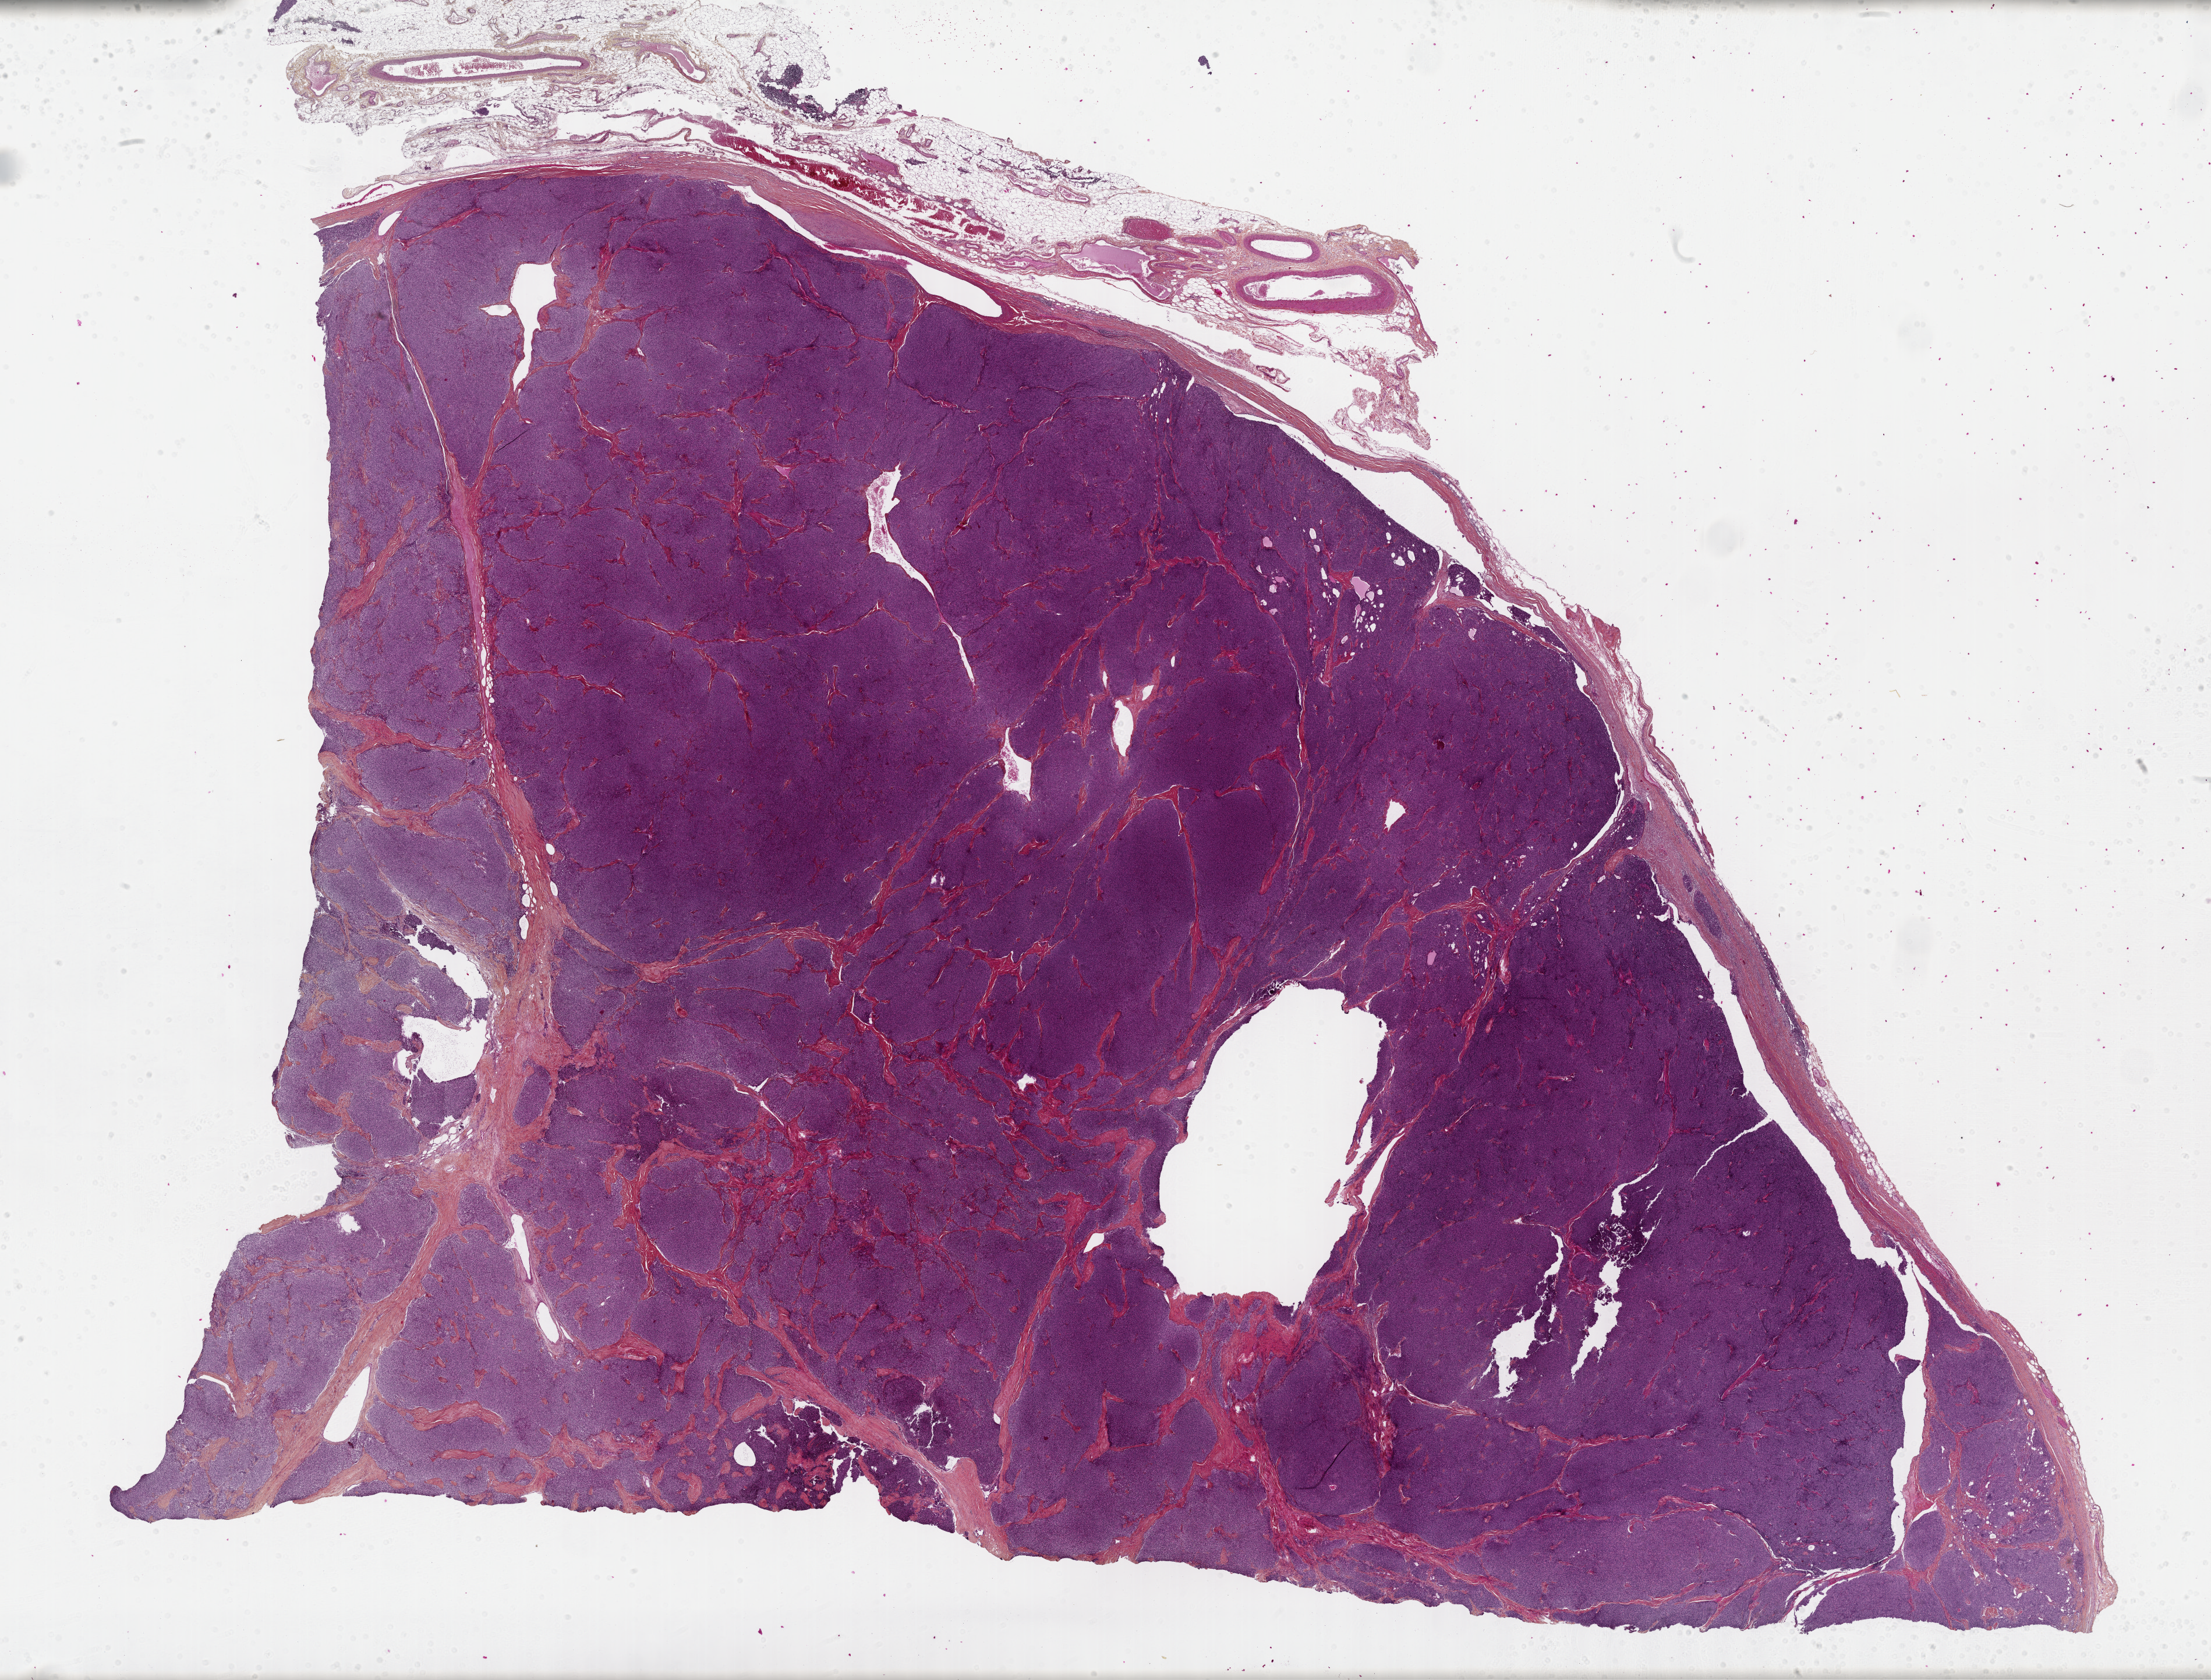
Whole-slide histology image, H&E-stained — shown as a low-resolution overview of the whole scanned area (about 30.7 x 23.3 mm), formalin-fixed paraffin-embedded (FFPE) diagnostic section, primary tumour sample from the thymus. Patient: female, age at initial diagnosis 58 years.
Pathologic diagnosis: Thymoma, type AB, malignant.